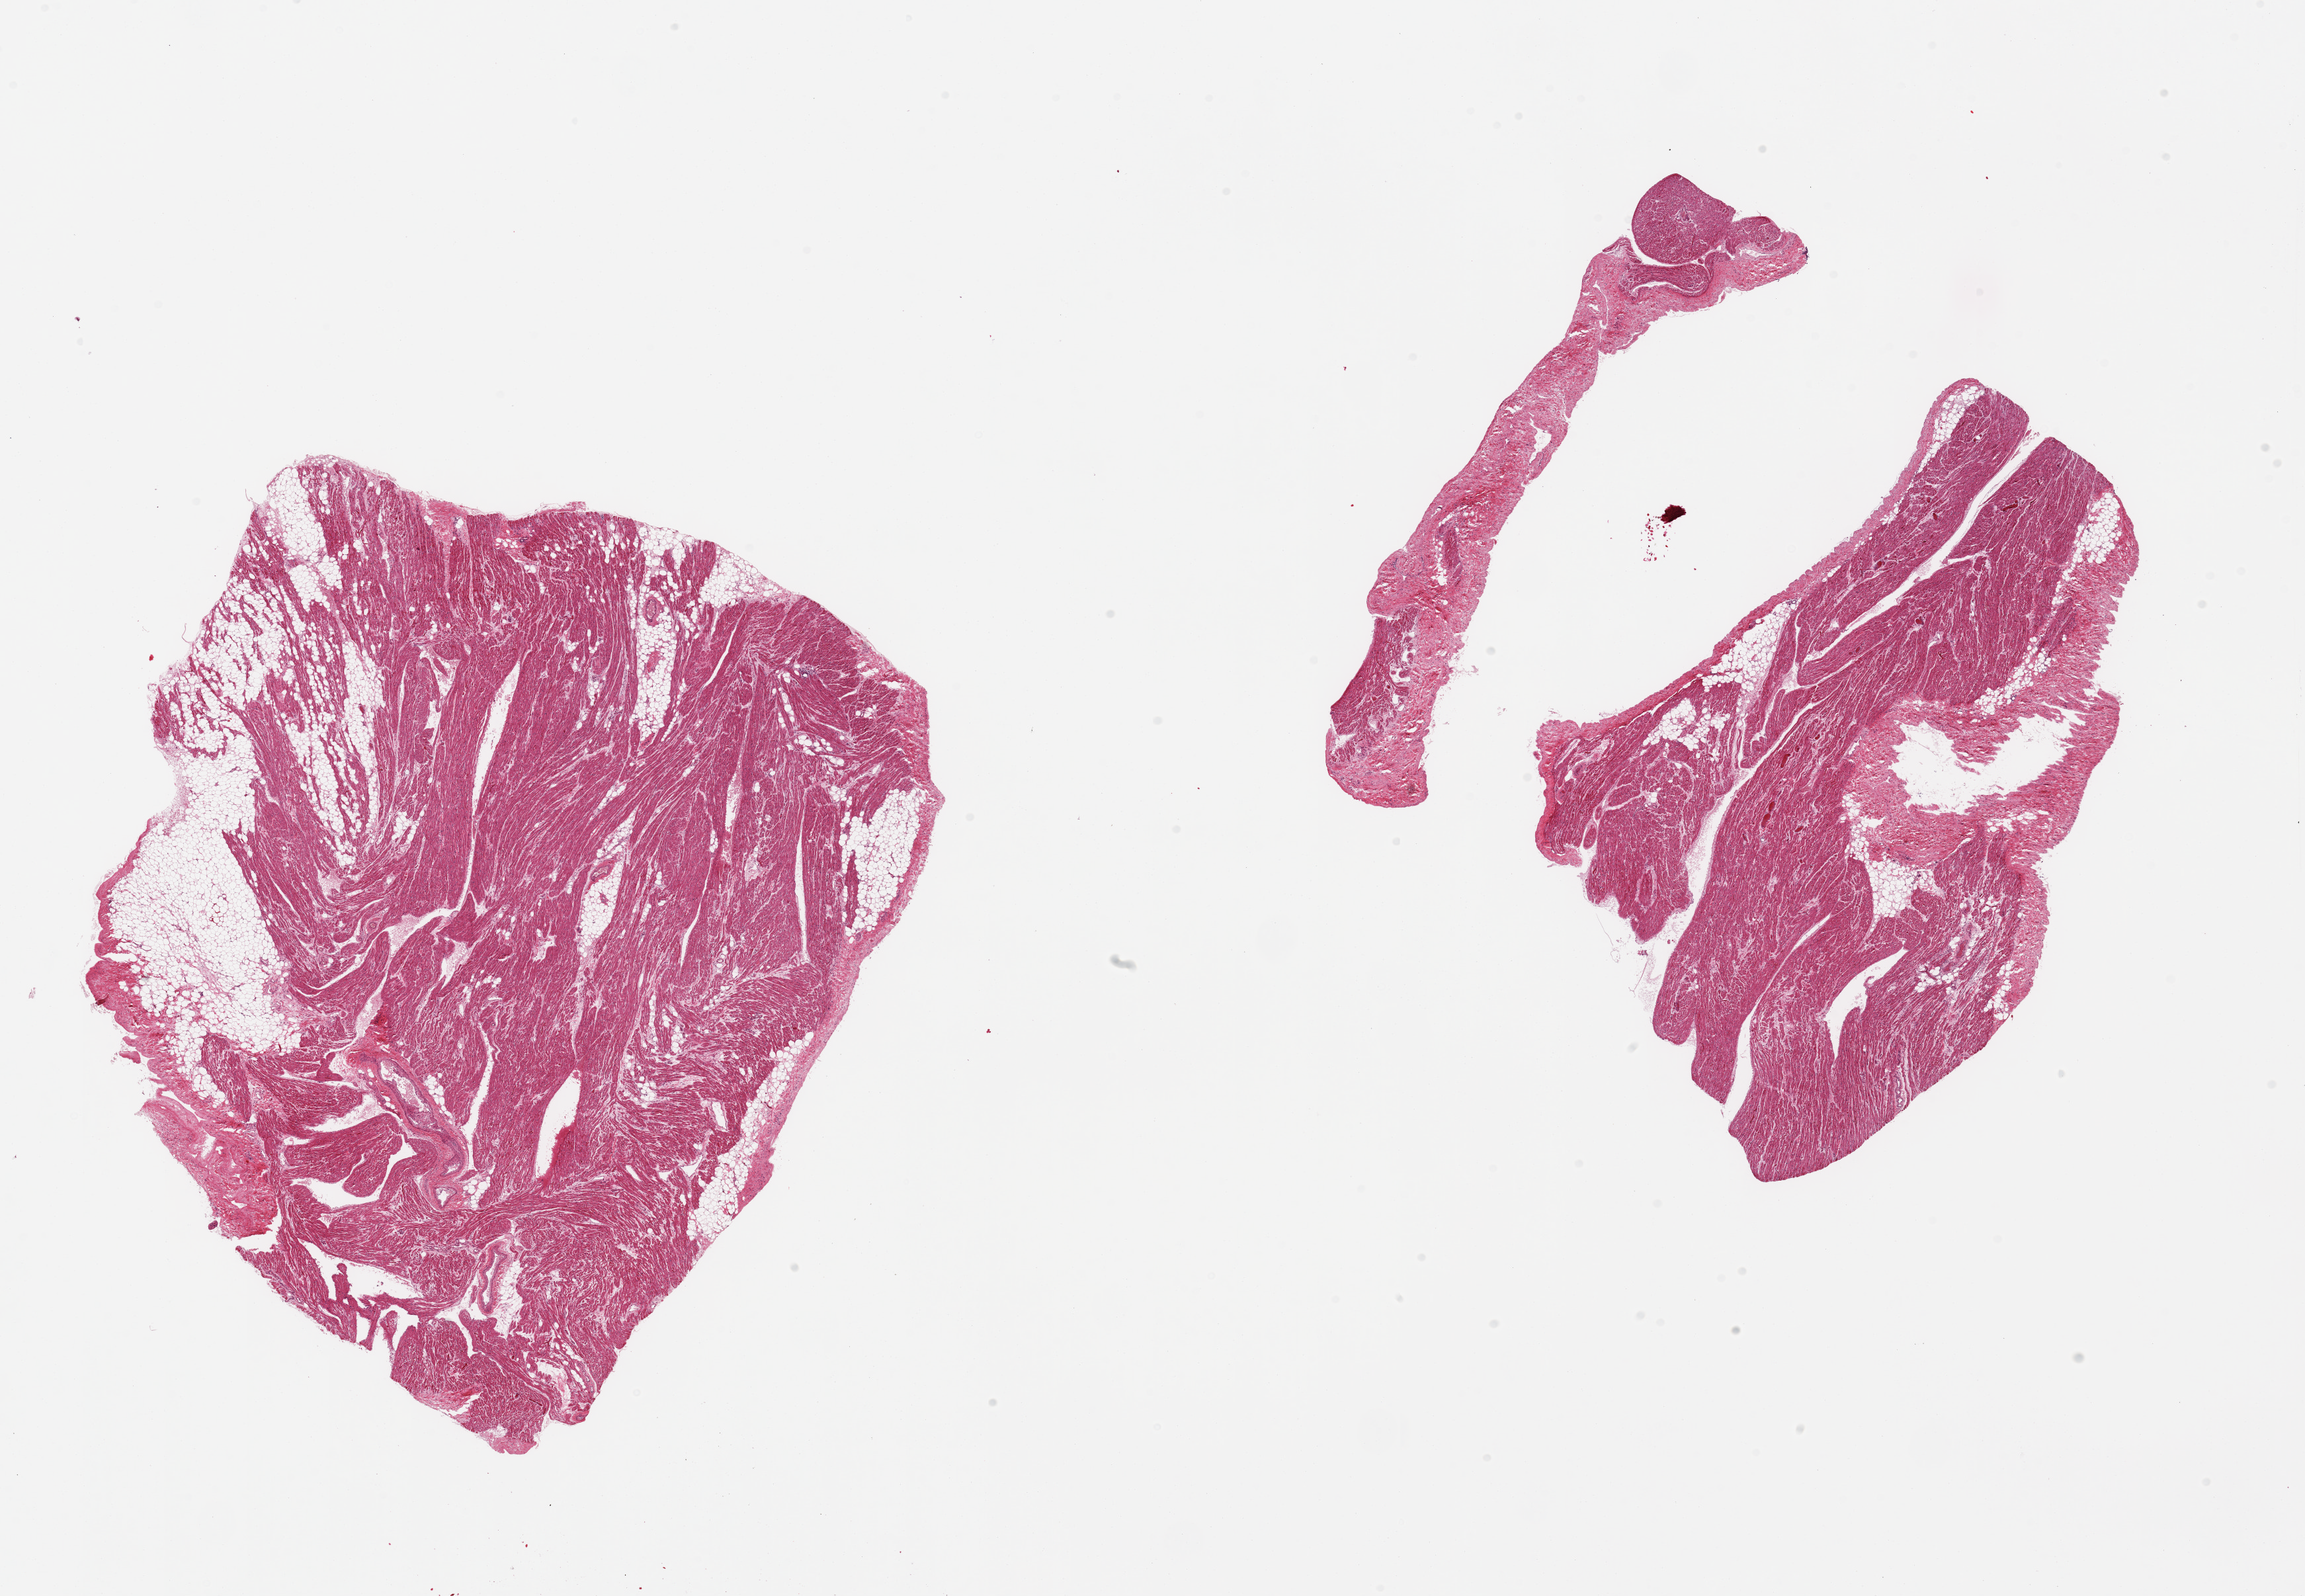
Hematoxylin and eosin (H&E) whole-slide image — shown as a low-resolution overview of the whole scanned area (about 27.6 x 19.1 mm), PAXgene-fixed paraffin-embedded (PFPE) section, section of auricular appendage (target tissue), tissue donor sample. Female donor.
Pathologist's review note for this sample: 2 pieces: 1 has 20% internal fat, other has 10%.